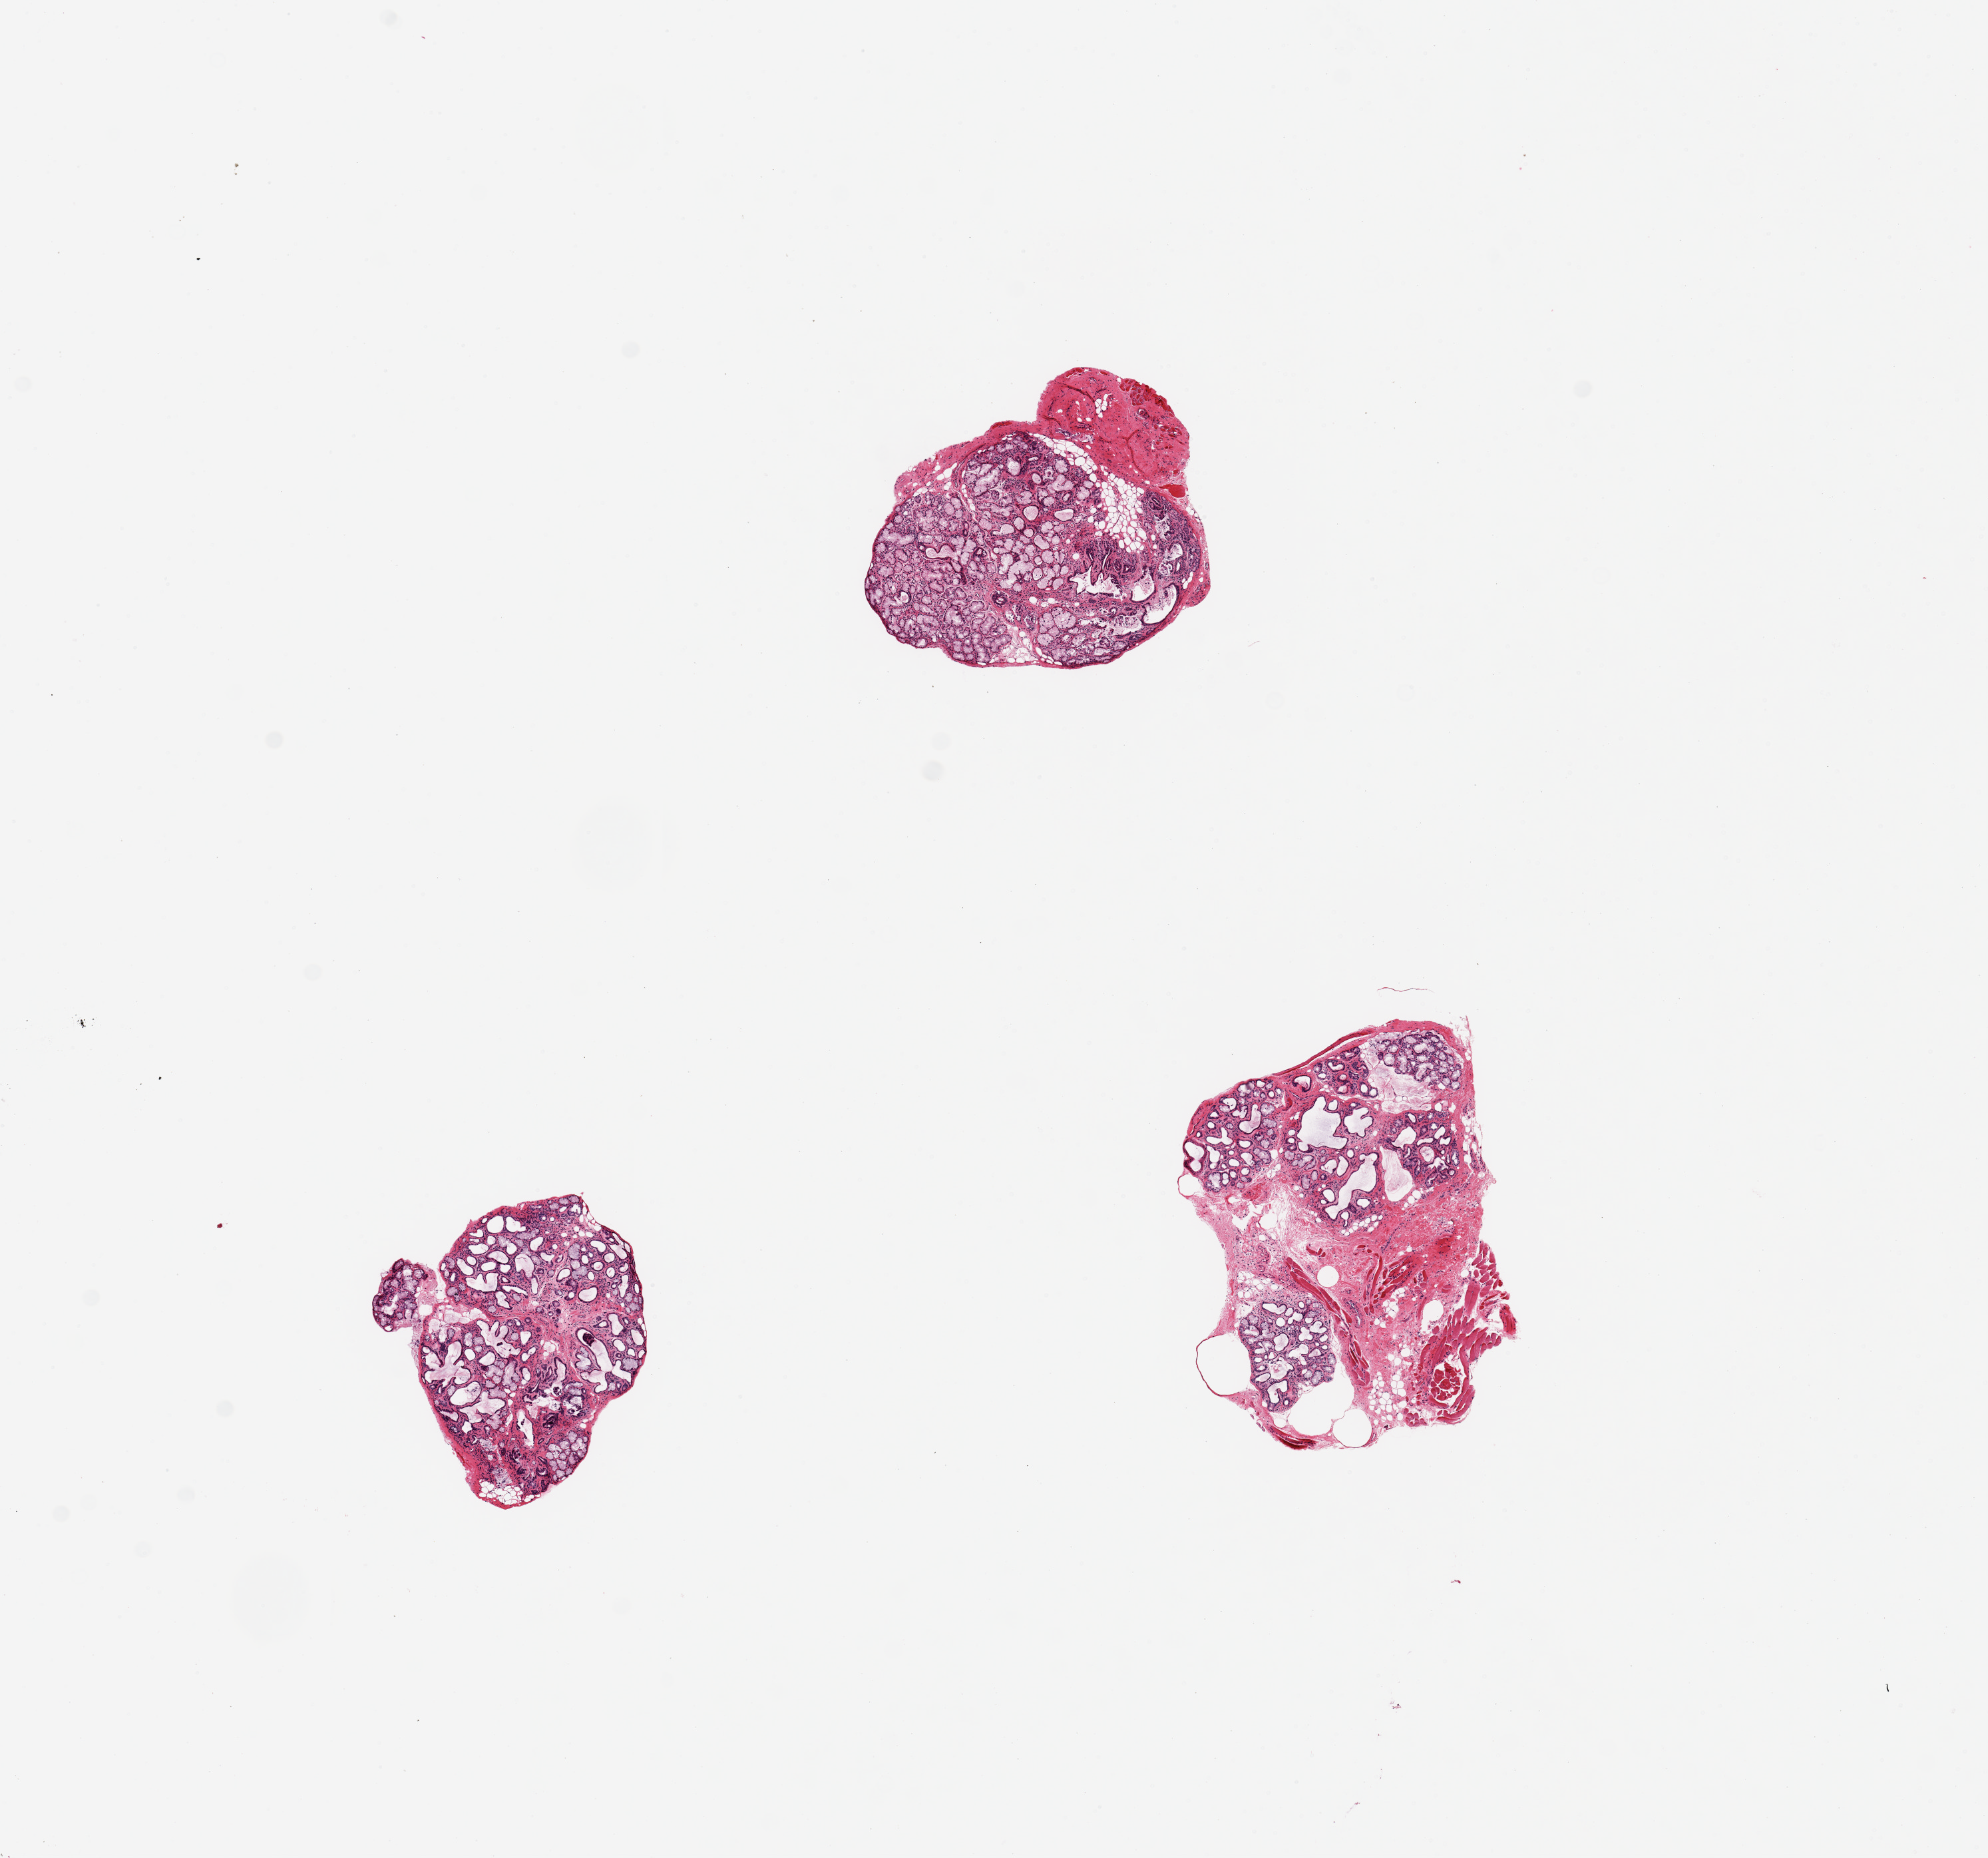
Digitized H&E-stained section, brightfield, shown as a low-resolution overview of the whole scanned area (about 11.8 x 11.0 mm). PAXgene-fixed, paraffin-embedded tissue. Target tissue: minor salivary gland. Donor tissue sample. Donor sex: male.
Review note (as recorded): 3 pieces, up to 3x2mm; severe gland atrophy and duct dilatation in one, moderate in 2nd, 3rd piece OK; very good dissection.